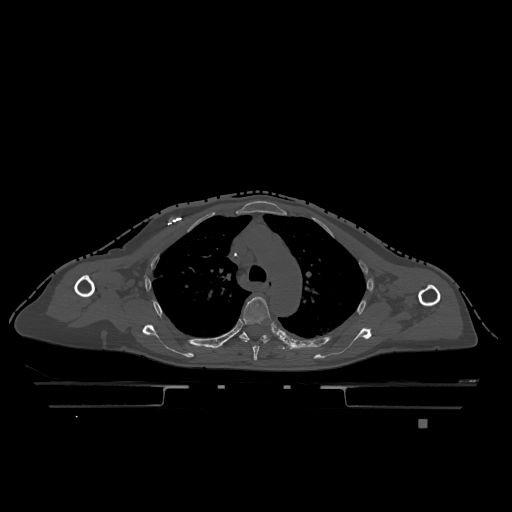
CT including the spine, one axial slice. Position 863 of 1317 along the scan axis. Bone window (W 1800 / L 400 HU). 0.5 mm slice thickness. 512 × 512 image matrix, field of view 500 × 500 mm. Female patient, age 74 years. Case-level facts recorded for this patient, not image findings: primary cancer: lung.
Outlined on this slice (semi-automatic segmentation, software-assisted and operator-edited):
- T4 vertebra: box from (x=240, y=297) to (x=272, y=361) px
- T5 vertebra: (x=239, y=332)–(x=285, y=350)